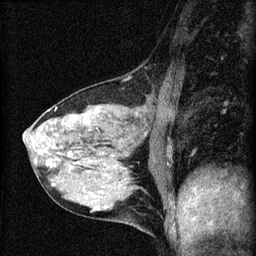
Breast MRI (dynamic contrast-enhanced), one sagittal slice; dynamic contrast-enhanced series, image 2 of 4 at this slice position (ordered by acquisition); 1.5 T; TE 4.2 ms, TR 8.2 ms; 2 mm slice thickness; 256 × 256 image matrix, field of view 180 × 180 mm. Female patient, age 41 years.
Annotated regions visible in this slice (semi-automatically segmented with operator editing):
- analysis volume of interest (the breast-tissue region the enhancement analysis was run in; not a lesion): bounding box [x1, y1, x2, y2] px = [23, 91, 166, 210]
- tumour enhancement mask (voxels above the 70 % enhancement threshold inside the analysis volume of interest): [33, 127, 98, 168]